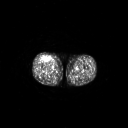
FDG PET of an extremity soft-tissue mass (from a PET/CT study), one axial slice. Slice 259 of 311 in the series (ordered by position). 3.27 mm slice thickness. 128 × 128 image matrix, field of view 700 × 700 mm. Patient: male, 56 years. From the clinical record (not read from this slice): histological type: pleiomorphic leiomyosarcoma; grade: intermediate; site of the primary tumour: right thigh.
Outlined on this slice (expert contour drawn on MRI and transferred to this co-registered scan by the dataset authors):
- gross tumour volume including surrounding oedema: bounding box <42,55,51,62> (left, top, right, bottom; pixels)